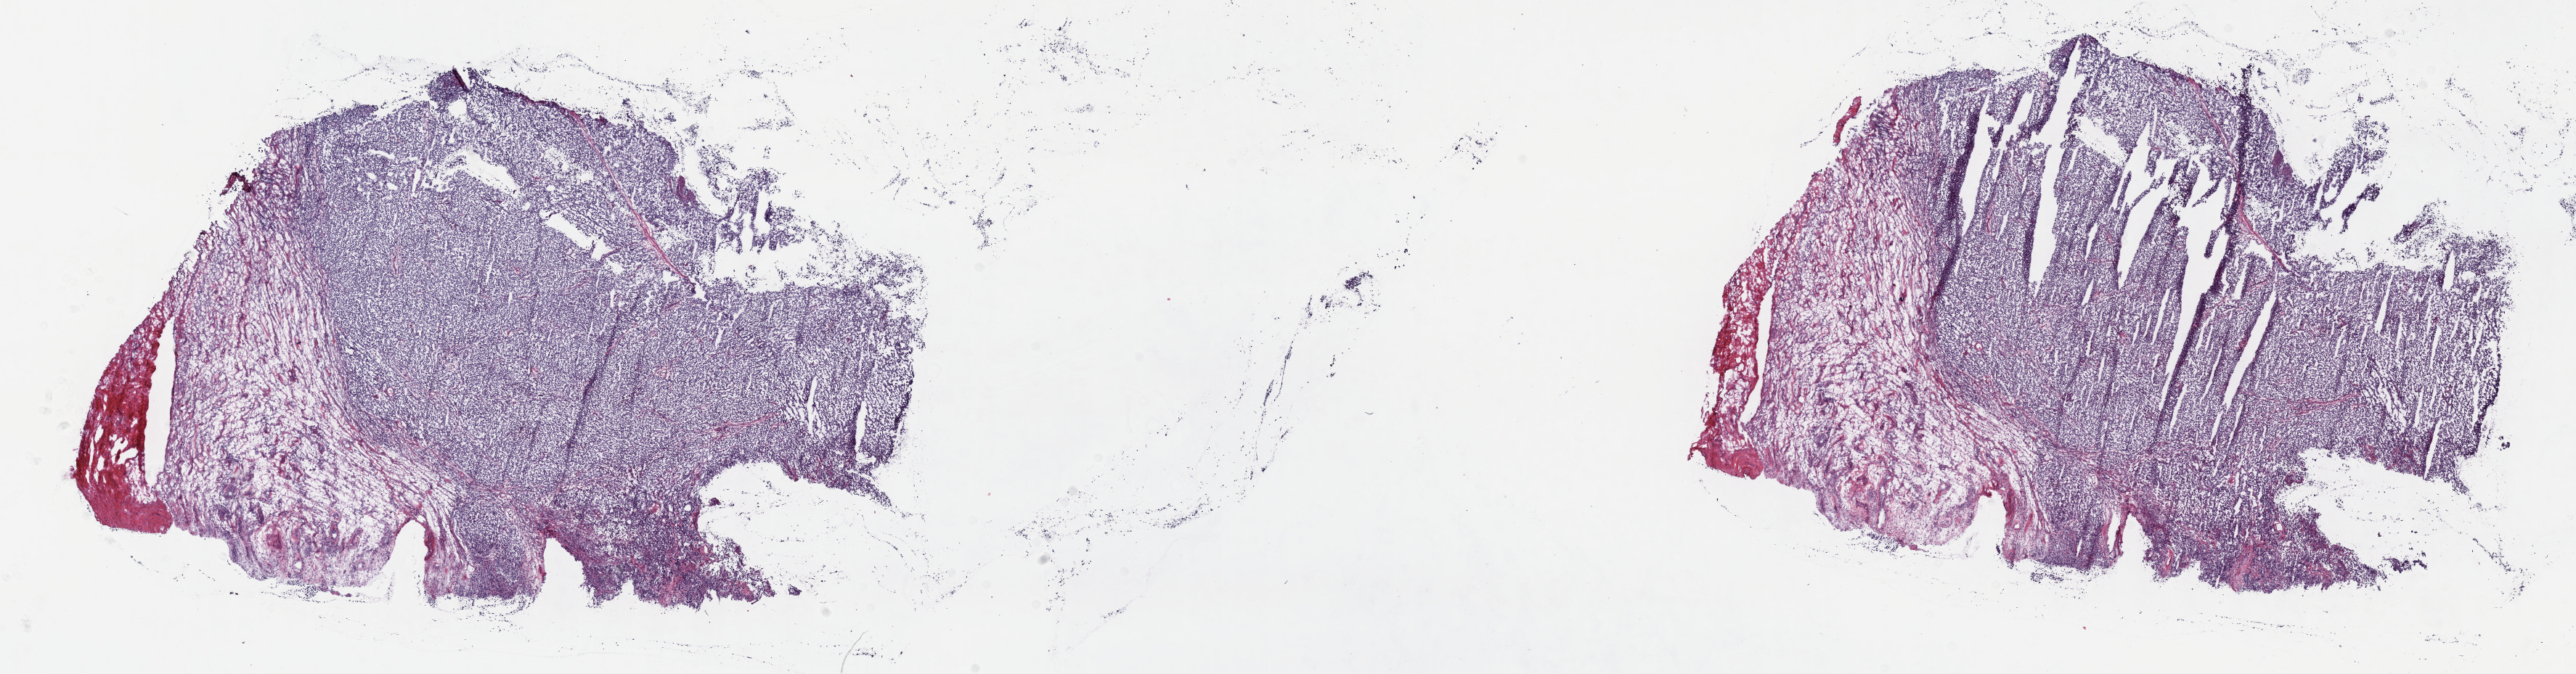
Whole-slide histology image, Hematoxylin and eosin (H&E) stained, whole scanned area (about 28.7 x 7.5 mm) shown as a low-resolution overview; frozen section from the top of the tissue portion; primary tumour sample from the testis. Patient: male, age at initial diagnosis 23 years. Slide review estimates, as recorded: tumour cells 70%, tumour nuclei 70%, normal cells 0%, stromal cells 20%, necrosis 10%. Infiltration values recorded for this section: lymphocyte infiltration 60%, monocyte infiltration 20%, neutrophil infiltration 20%.
• laterality: right
• AJCC pathologic stage: I (6th edition)
• diagnosis: Seminoma, NOS